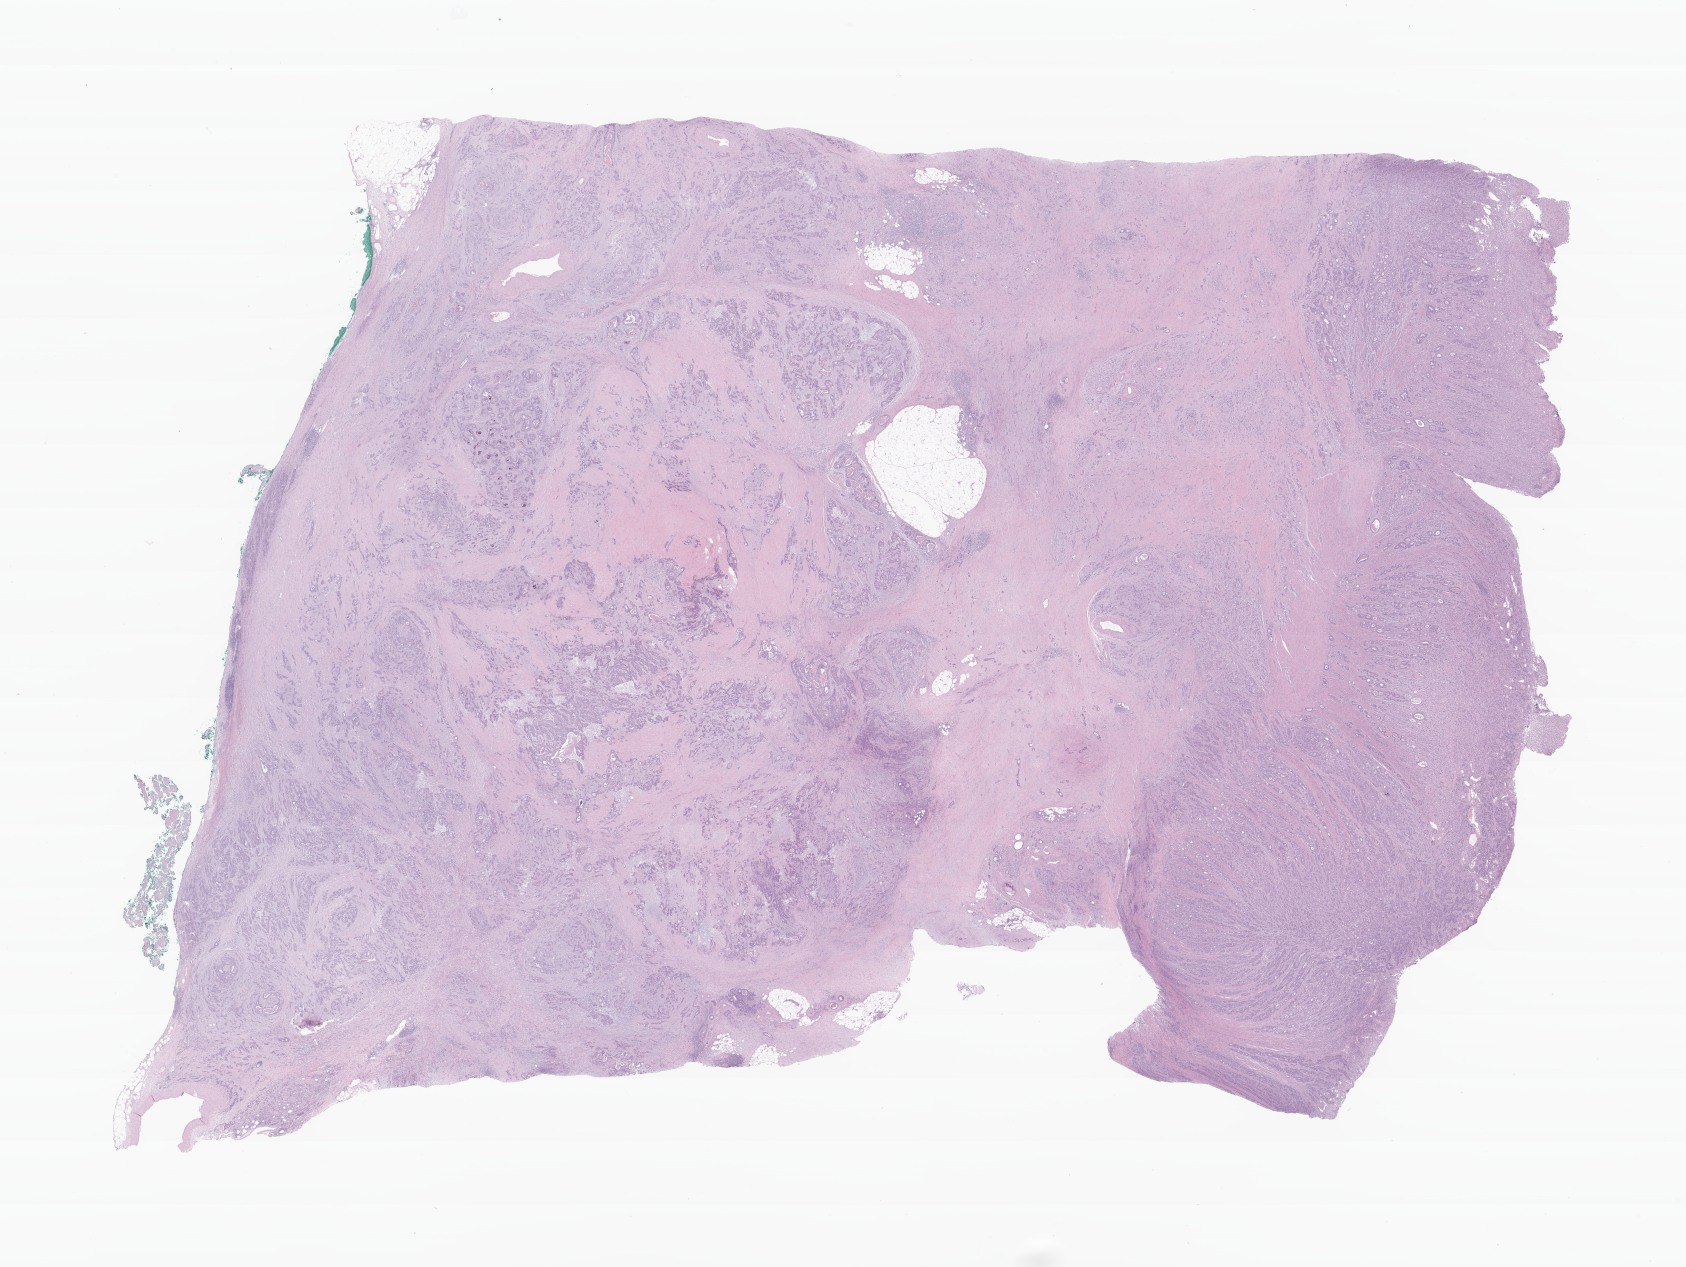
Whole-slide image, haematoxylin and eosin stain of tumor tissue from the colon, low-resolution overview of the scanned area, about 28.4 x 21.3 mm, formalin-fixed, paraffin-embedded (FFPE) tissue. Patient: female, age 211 months.
* diagnosis: Adenocarcinoma, NOS